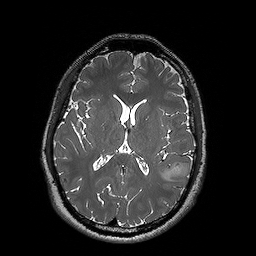
Brain MRI from a brain-tumour surgery series, one axial slice; position 80 of 192 along the scan axis; 1 mm slice thickness; 256 × 256 image matrix, field of view 250 × 250 mm. From the clinical record (not read from this slice): histopathology: Oligodendroglioma; WHO grade: 2; IDH mutation: yes.
Annotated regions visible in this slice (outlined manually by an expert reader):
- tumour: box from (x=159, y=162) to (x=193, y=181) px